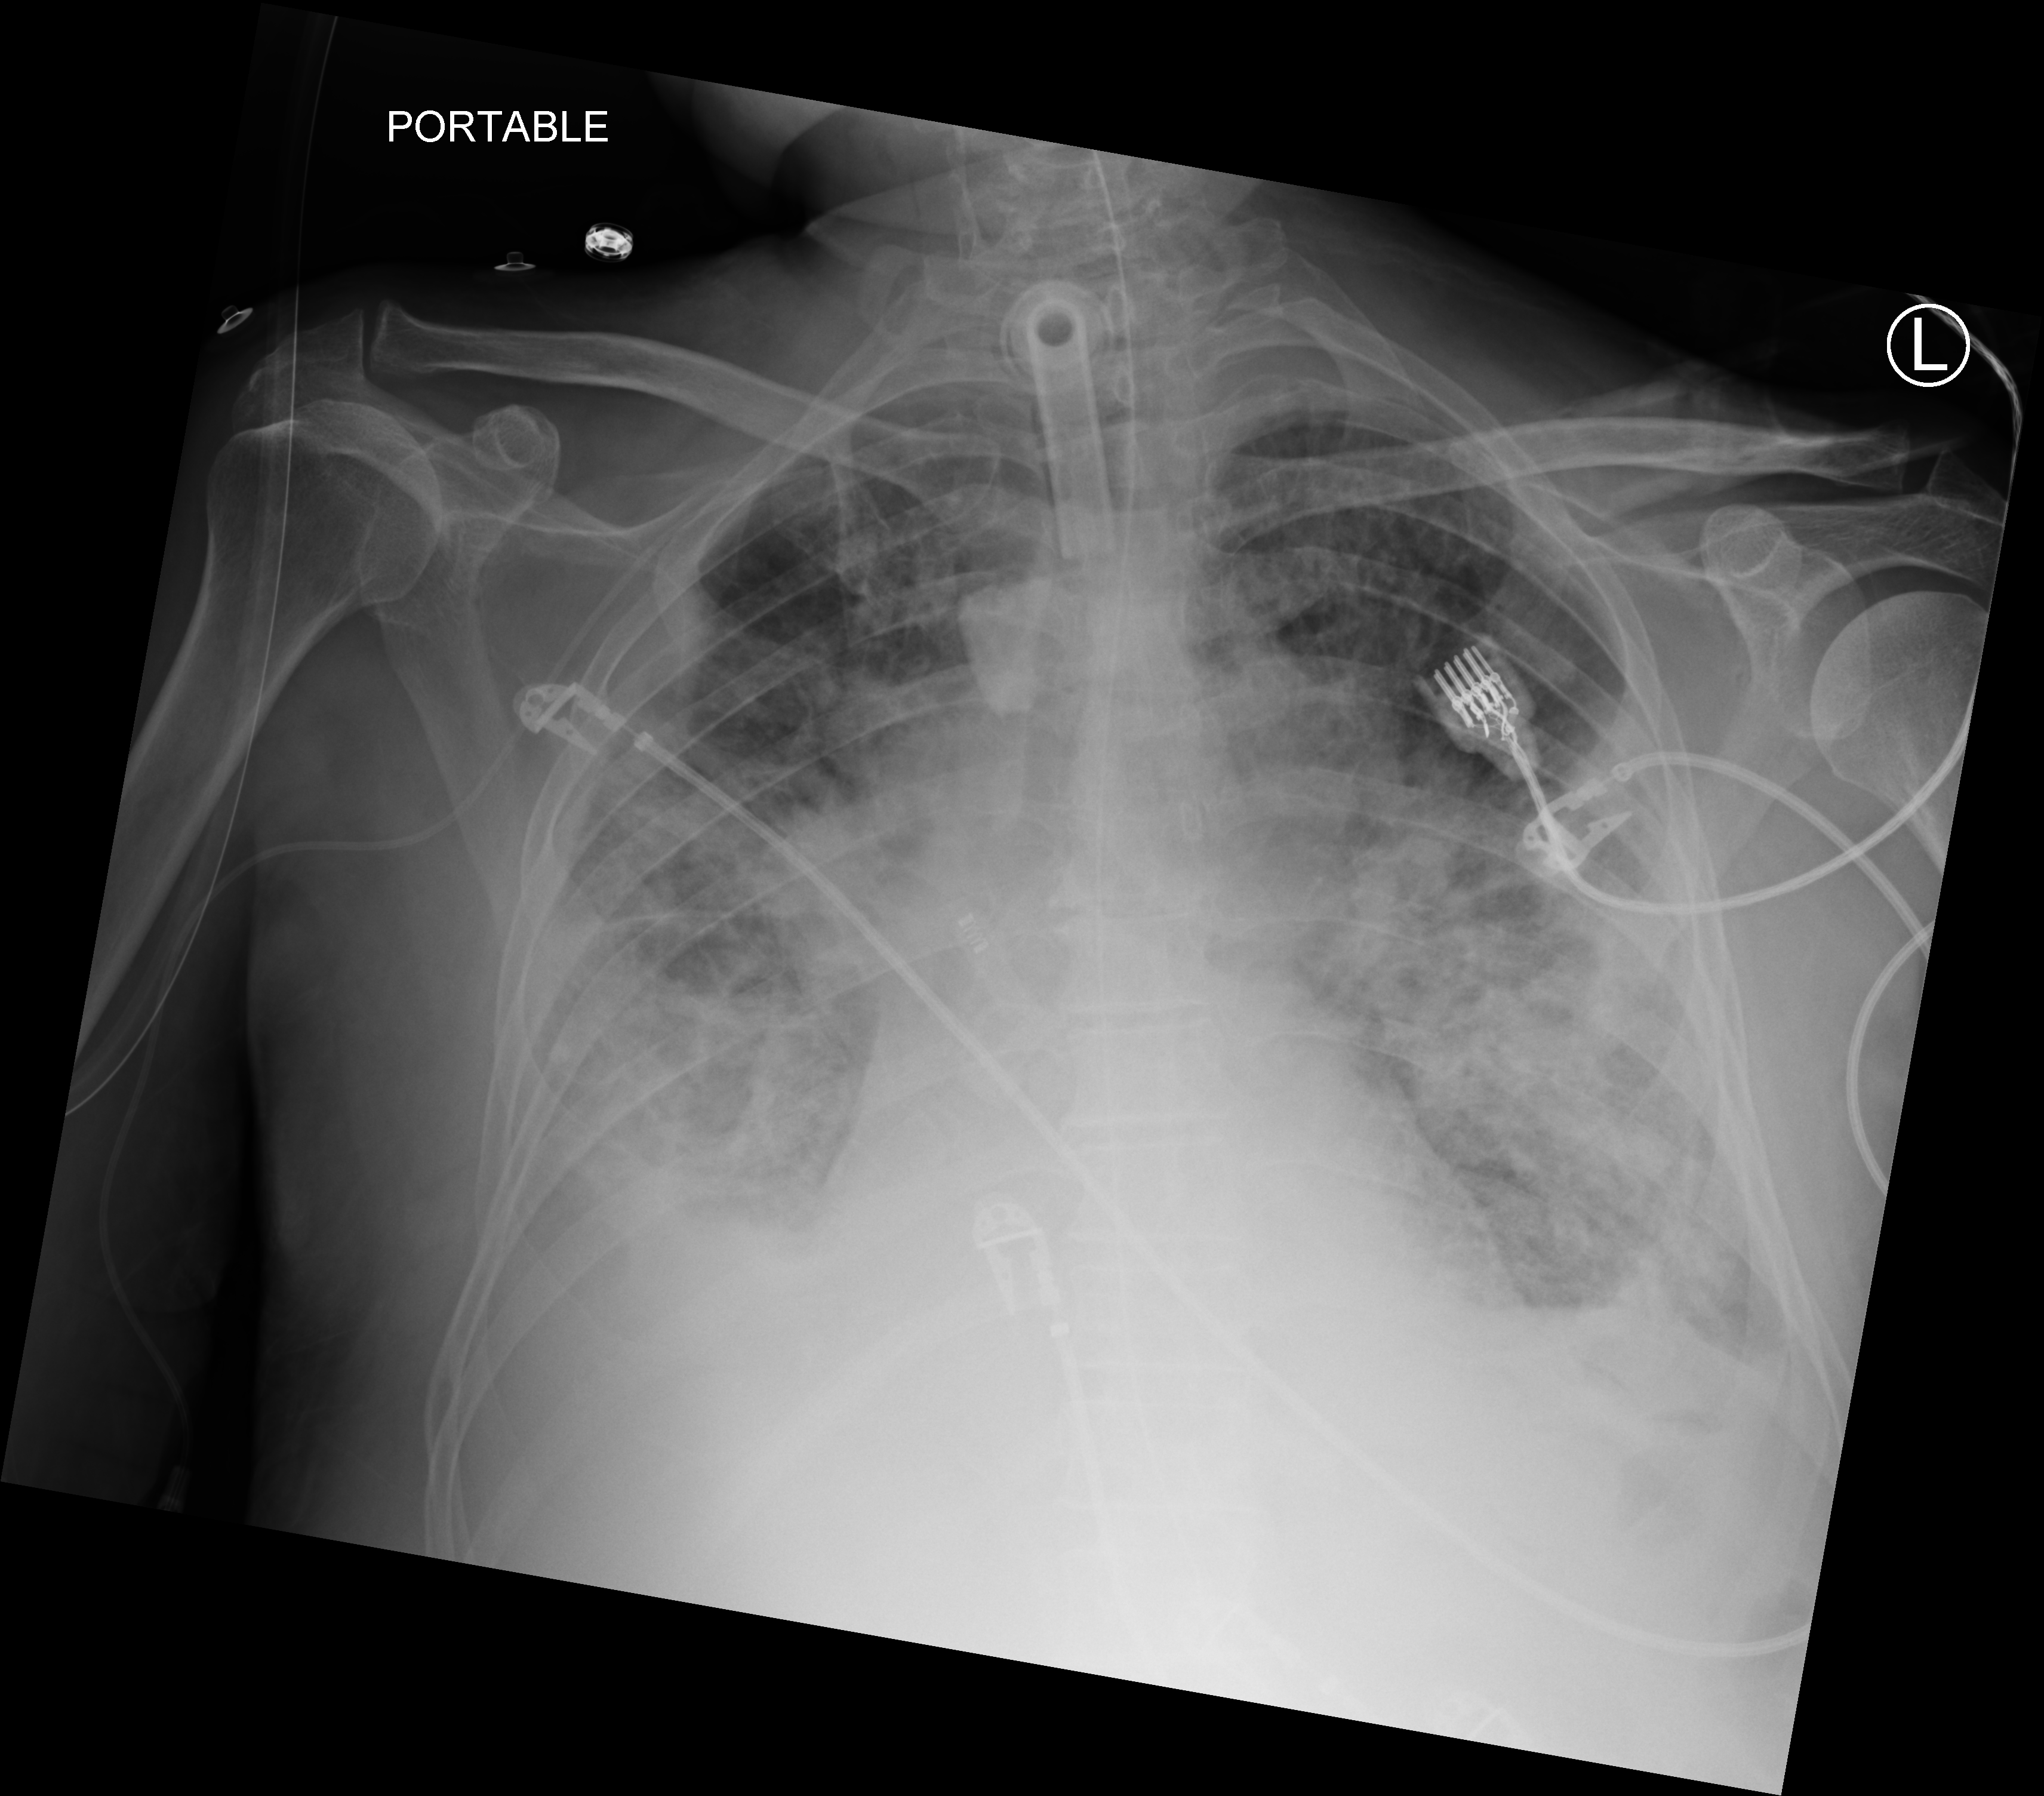
Bedside chest radiograph (computed radiography). Male patient hospitalised with COVID-19, age 75–90 years.
From the hospital-stay record, not from the radiograph (when in the stay this image was taken is not recorded):
- admitted to intensive care during this hospital stay: yes
- chronic kidney disease (admission record): no
- mechanically ventilated during this hospital stay: yes